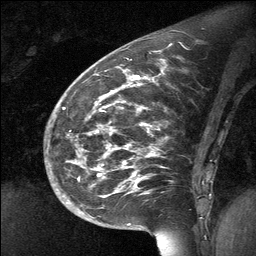
Breast MRI (dynamic contrast-enhanced), one sagittal slice; position 24 of 64 along the scan axis; dynamic contrast-enhanced study with each time point stored as its own series, time point 2 of 3 at this slice position (early post-contrast, ordered by acquisition time); 1.5 T; TE 4.8 ms, TR 27 ms; 2 mm slice thickness; 256 × 256 image matrix, field of view 200 × 200 mm. Patient: female, 39 years. From the clinical record (not read from this slice): setting: breast cancer imaged before/during neoadjuvant chemotherapy; receptor status: HER2-positive.
Structures marked on this image (semi-automatically segmented with operator editing):
- analysis volume of interest (the breast-tissue region the enhancement analysis was run in; not a lesion): box from (x=70, y=69) to (x=202, y=224) px
- tumour enhancement mask (voxels above the 90 % enhancement threshold inside the analysis volume of interest): (x=96, y=76)–(x=140, y=133)